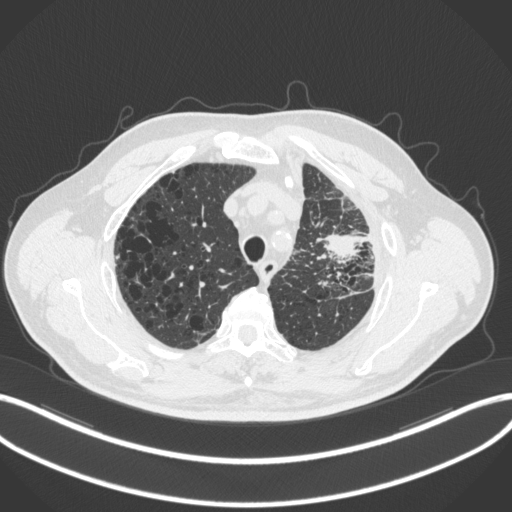
Chest CT, one axial slice. Position 246 of 286 along the scan axis. Reconstruction kernel B31f. 120 kVp. Lung window (W 1500 / L -600 HU). 1 mm slice thickness. 512 × 512 image matrix, field of view 400 × 400 mm. Male patient, age 68 years. Case-level facts recorded for this patient, not image findings: clinical TNM (as recorded): T3 N3 M1.
Structures marked on this image (rectangle marked by the reading radiologist):
- lung tumour (recorded histology: adenocarcinoma): bounding box [x1, y1, x2, y2] px = [315, 229, 362, 268]